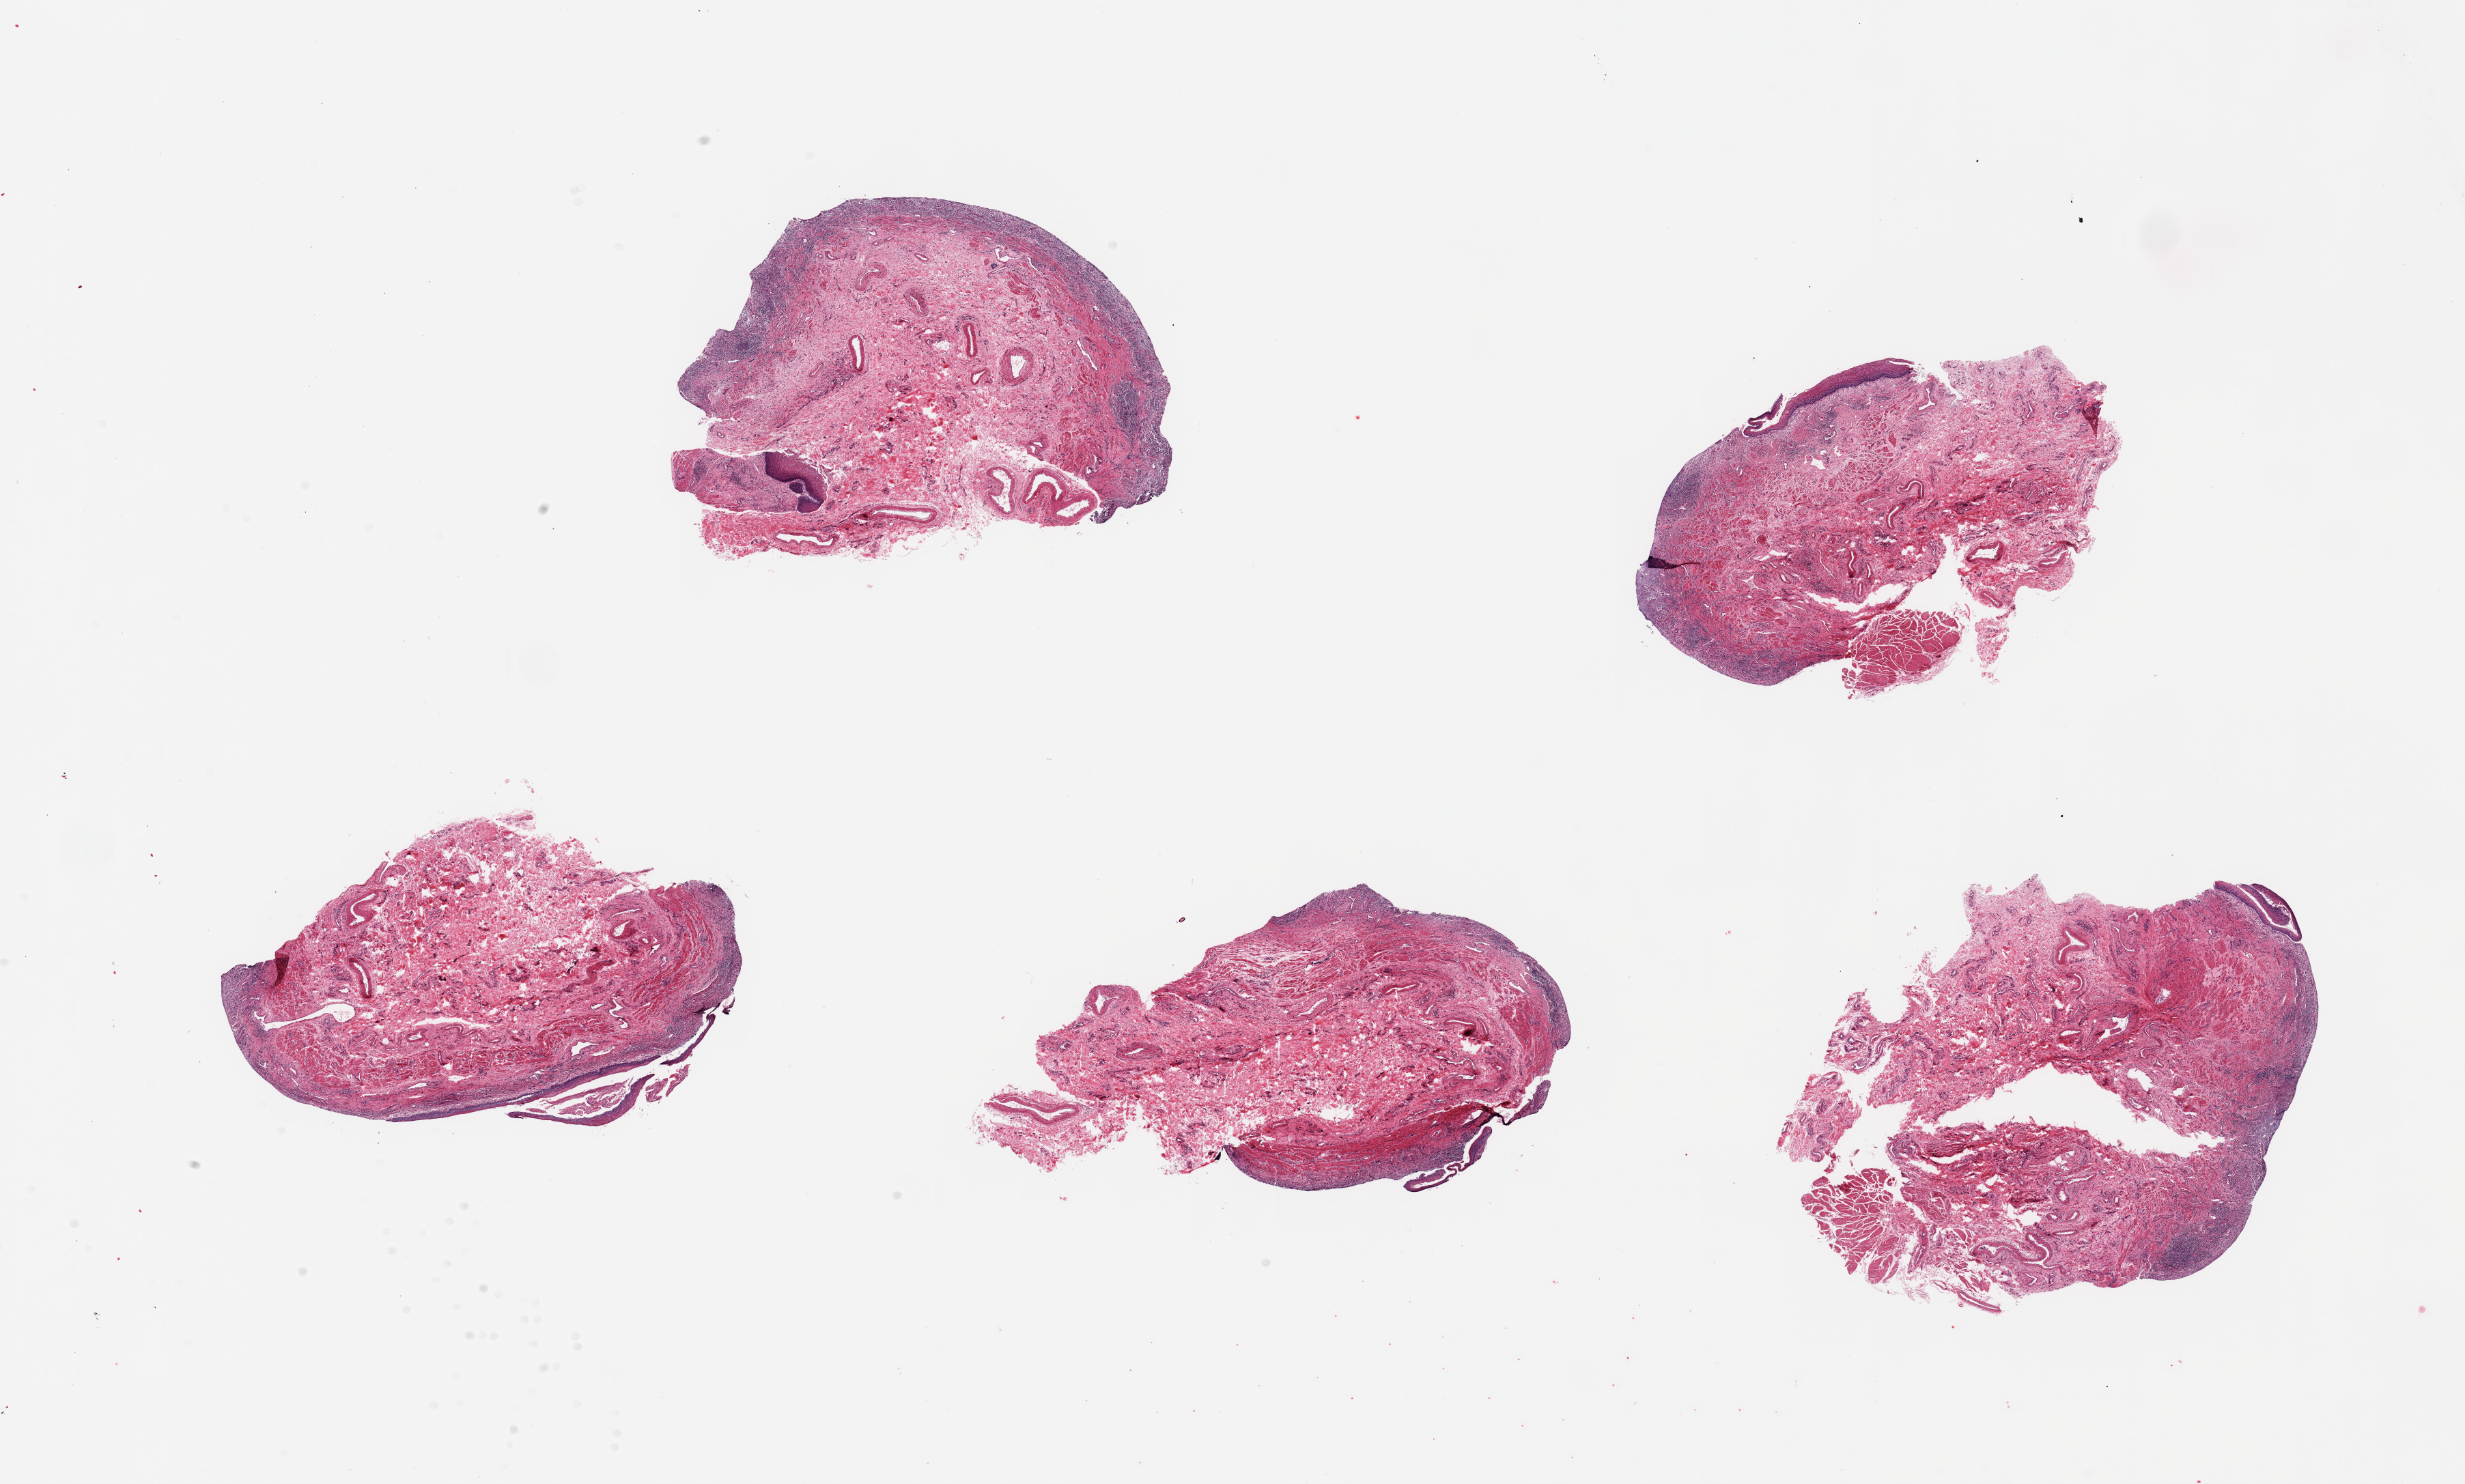
Haematoxylin and eosin whole-slide image, shown as a low-resolution overview of the whole scanned area (about 28.5 x 17.2 mm, acquisition: 20x scan), PAXgene-fixed, paraffin-embedded tissue, sampled site (target tissue): esophageal mucous membrane, tissue donor sample.
Reviewer comment on this tissue sample: 5 pieces; severe erosive esophagitis with limited intact squamous epithelium, few fragments of muscularis.